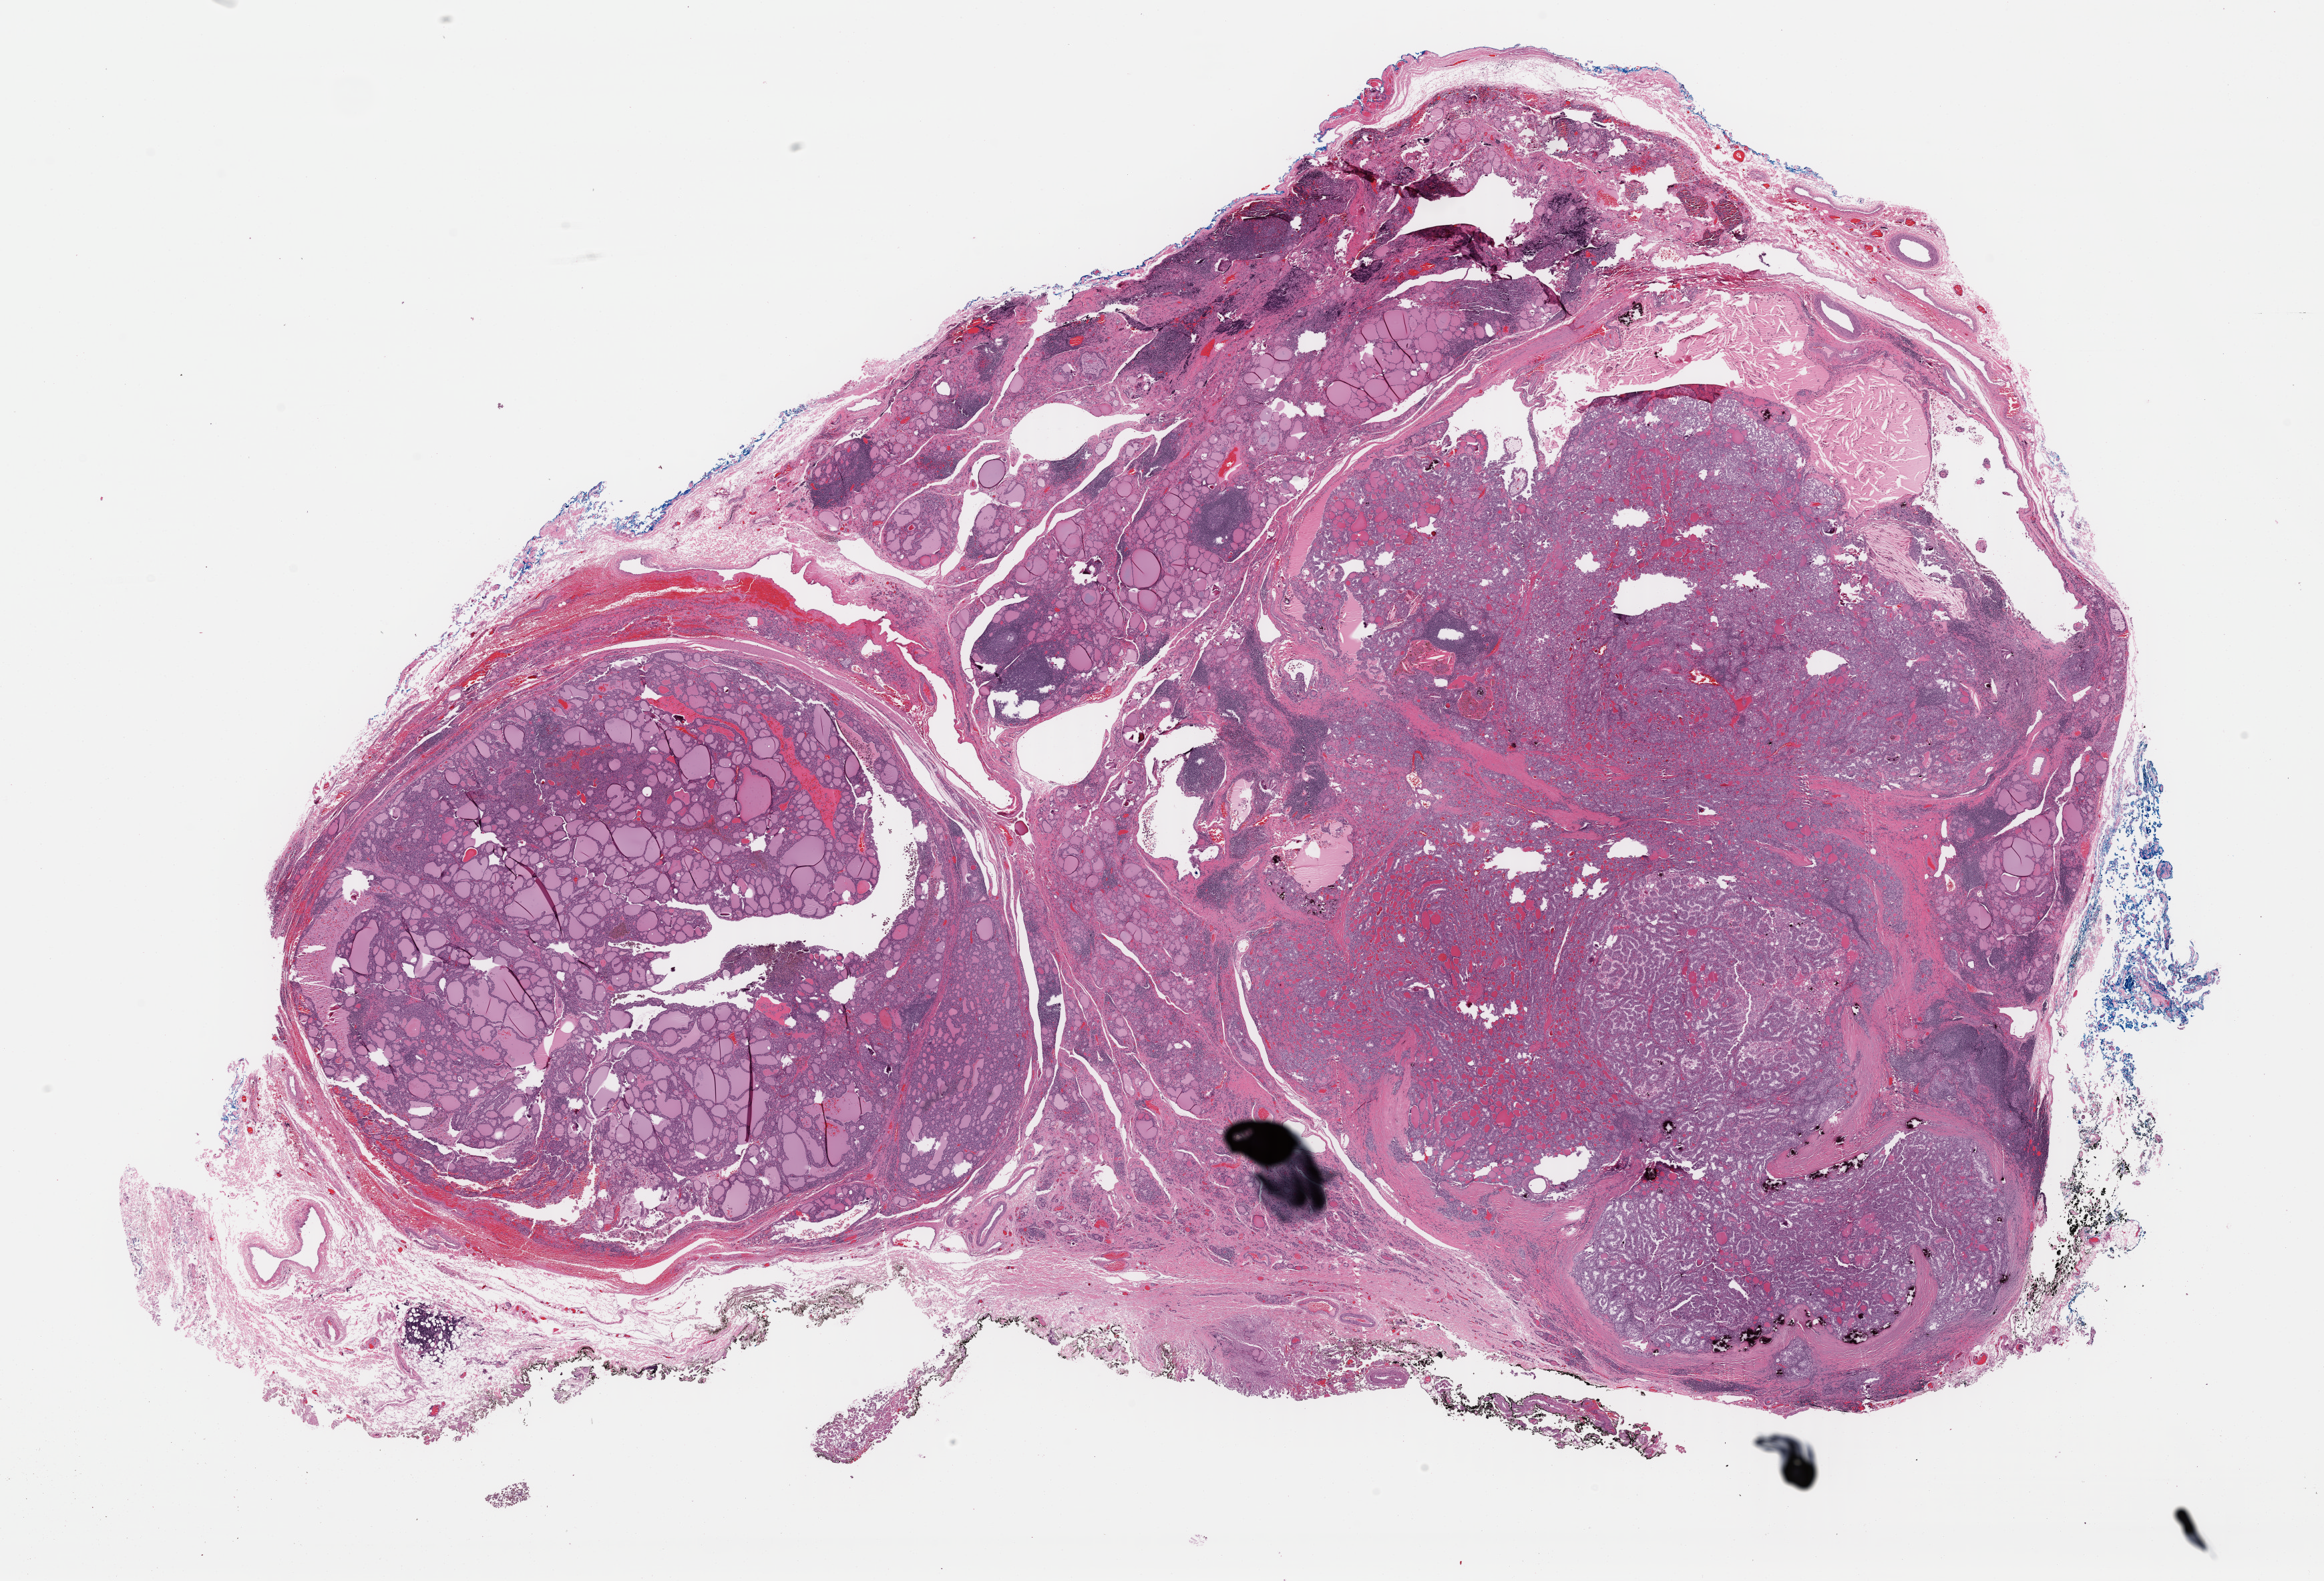
H&E whole-slide image — whole scanned area (about 27.5 x 18.7 mm, slide scanned at 40x) shown as a low-resolution overview; FFPE section; thyroid, primary tumour sample. Female patient; age at initial diagnosis 57 years.
Diagnosis: Papillary adenocarcinoma, NOS (thyroid gland).